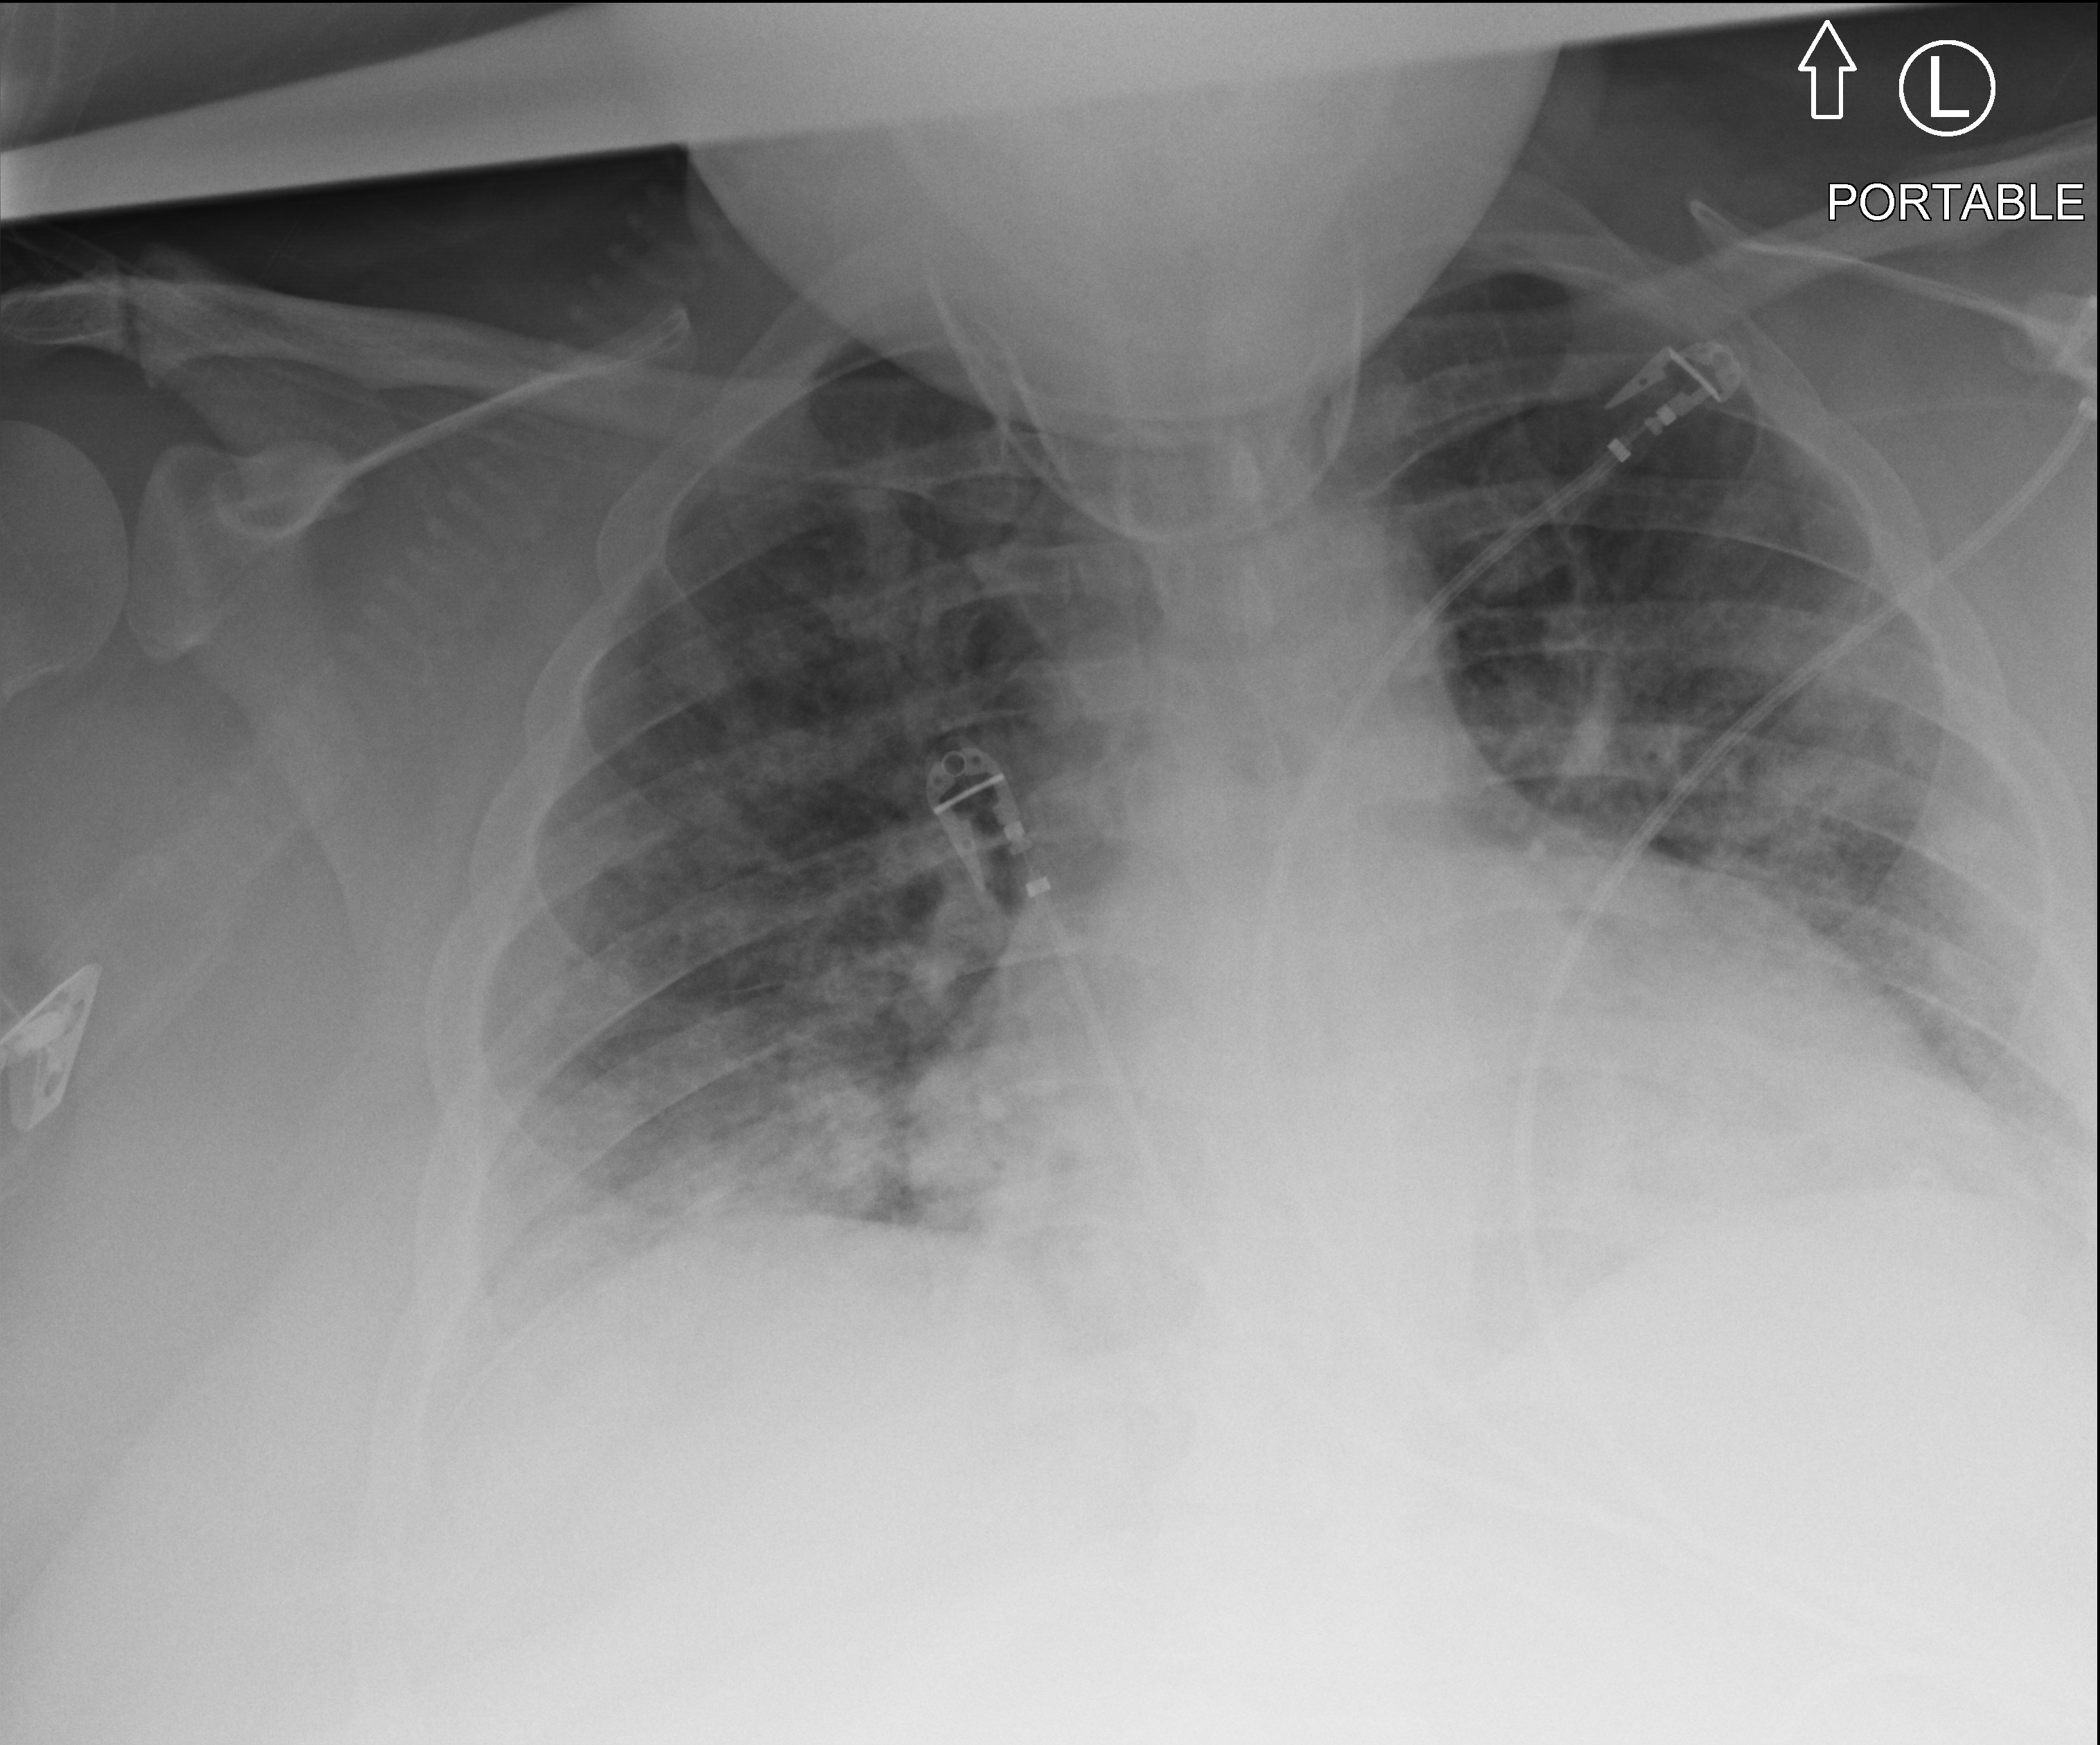
Bedside chest radiograph (computed radiography); anteroposterior (AP) projection. Patient hospitalised with COVID-19; male, aged 18–59 years.
From the hospital-stay record, not from the radiograph (when in the stay this image was taken is not recorded): admitted to intensive care during this hospital stay: yes; mechanically ventilated during this hospital stay: no.